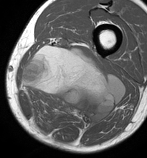
MRI of an extremity soft-tissue mass, one axial slice; slice 39 of 86 in the series (ordered by position); MR volume resampled by the dataset authors to the PET/CT grid (not the native acquisition matrix); 3.27 mm slice thickness; 147 × 158 image matrix. Male patient. Case-level facts recorded for this patient, not image findings: histological type: undifferentiated pleomorphic liposarcoma; grade: high; site of the primary tumour: left thigh.
Outlined on this slice (expert contour drawn on MRI and transferred to this co-registered scan by the dataset authors):
- gross tumour volume including surrounding oedema: box from (x=21, y=46) to (x=125, y=127) px
- gross tumour volume (mass): (x=21, y=46)–(x=125, y=127)